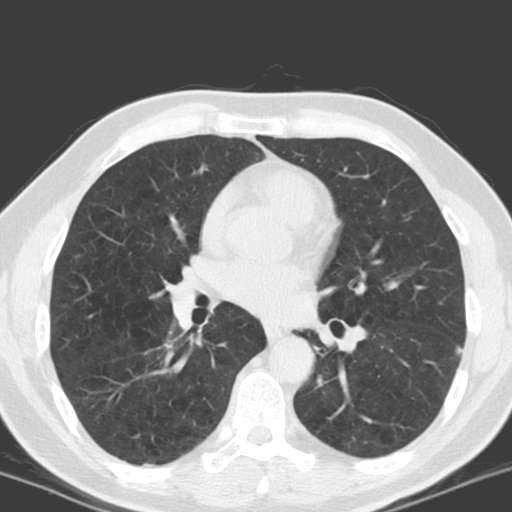
Chest CT (low-dose screening protocol), one axial image. First (baseline) screen. Lung window (W 1500 / L -600 HU). Male, age 57 years at enrolment. Former smoker at enrolment.
- Lesion marked by an expert reader, box from (x=437, y=333) to (x=473, y=365) px.
- Reader record for this screening exam (exam-level; its link to the box is not recorded): non-calcified nodule or mass ≥4 mm, left lower lobe, 8 × 5 mm, poorly defined margins, ground glass attenuation.
- Official screen result: positive, change unspecified: nodule(s) >= 4 mm or enlarging nodule(s), mass(es), or other non-specific abnormalities suspicious for lung cancer.
- Lung cancer was diagnosed 816 days after this screen: non-small cell carcinoma, left lower lobe, stage IV (AJCC 6th edition), 13 mm at pathology.